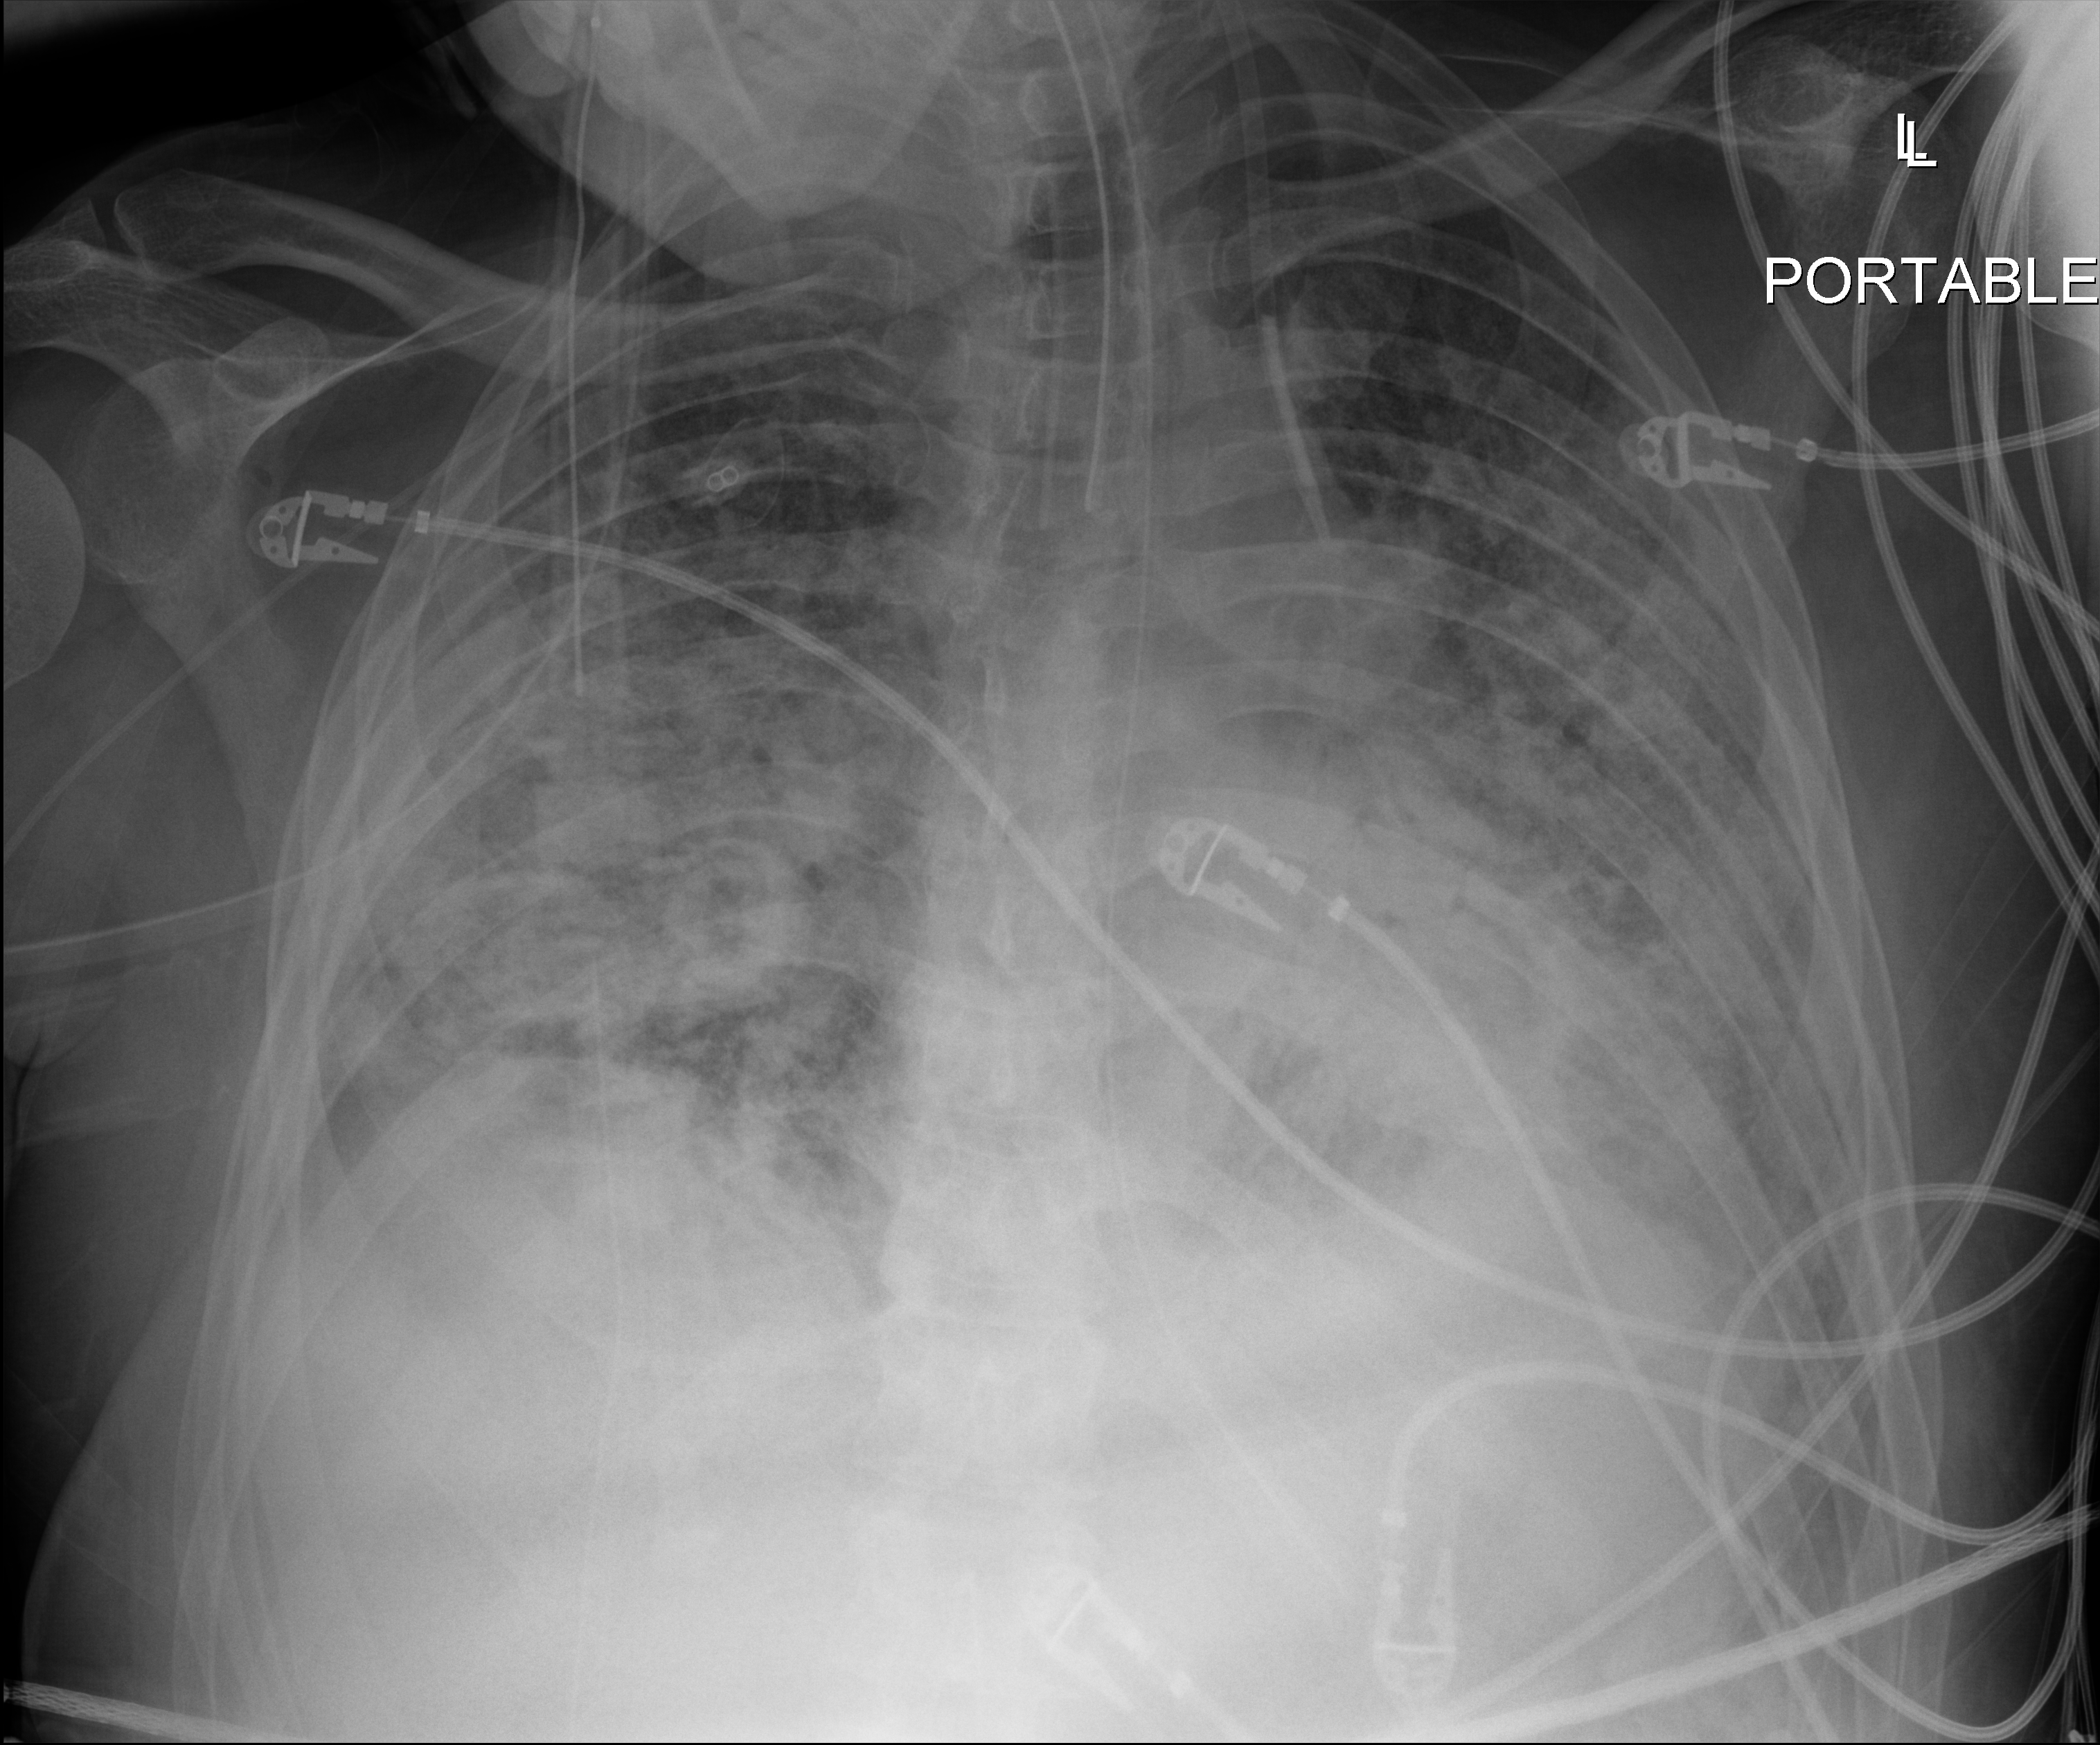
Chest radiograph (digital radiography); anteroposterior (AP) projection. Male patient hospitalised with COVID-19, age 18–59 years.
Admission-level facts for this patient (not findings on this image; timing relative to this image not recorded):
- admitted to intensive care during this hospital stay: yes
- diabetes (admission record): no